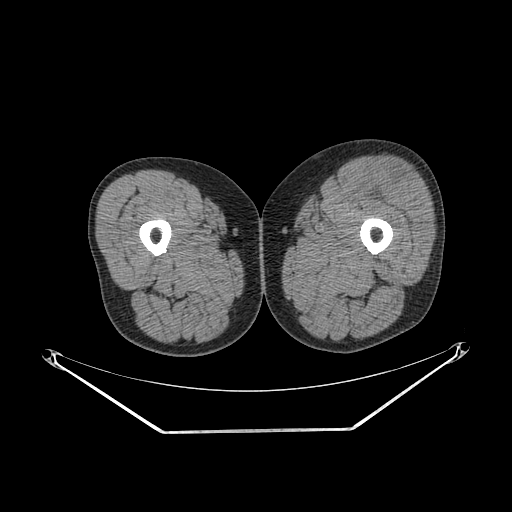
CT of an extremity soft-tissue mass (from a PET/CT study), one axial slice. Slice 224 of 267 in the series (ordered by position). 140 kVp. Soft-tissue window (W 400 / L 40 HU). 512 × 512 image matrix, field of view 500 × 500 mm. Male patient. Case-level facts recorded for this patient, not image findings: histological type: extraskeletal osteosarcoma; grade: high; site of the primary tumour: thigh.
Structures marked on this image (expert contour drawn on MRI and transferred to this co-registered scan by the dataset authors):
- gross tumour volume (mass): bounding box [x1, y1, x2, y2] px = [372, 167, 417, 204]